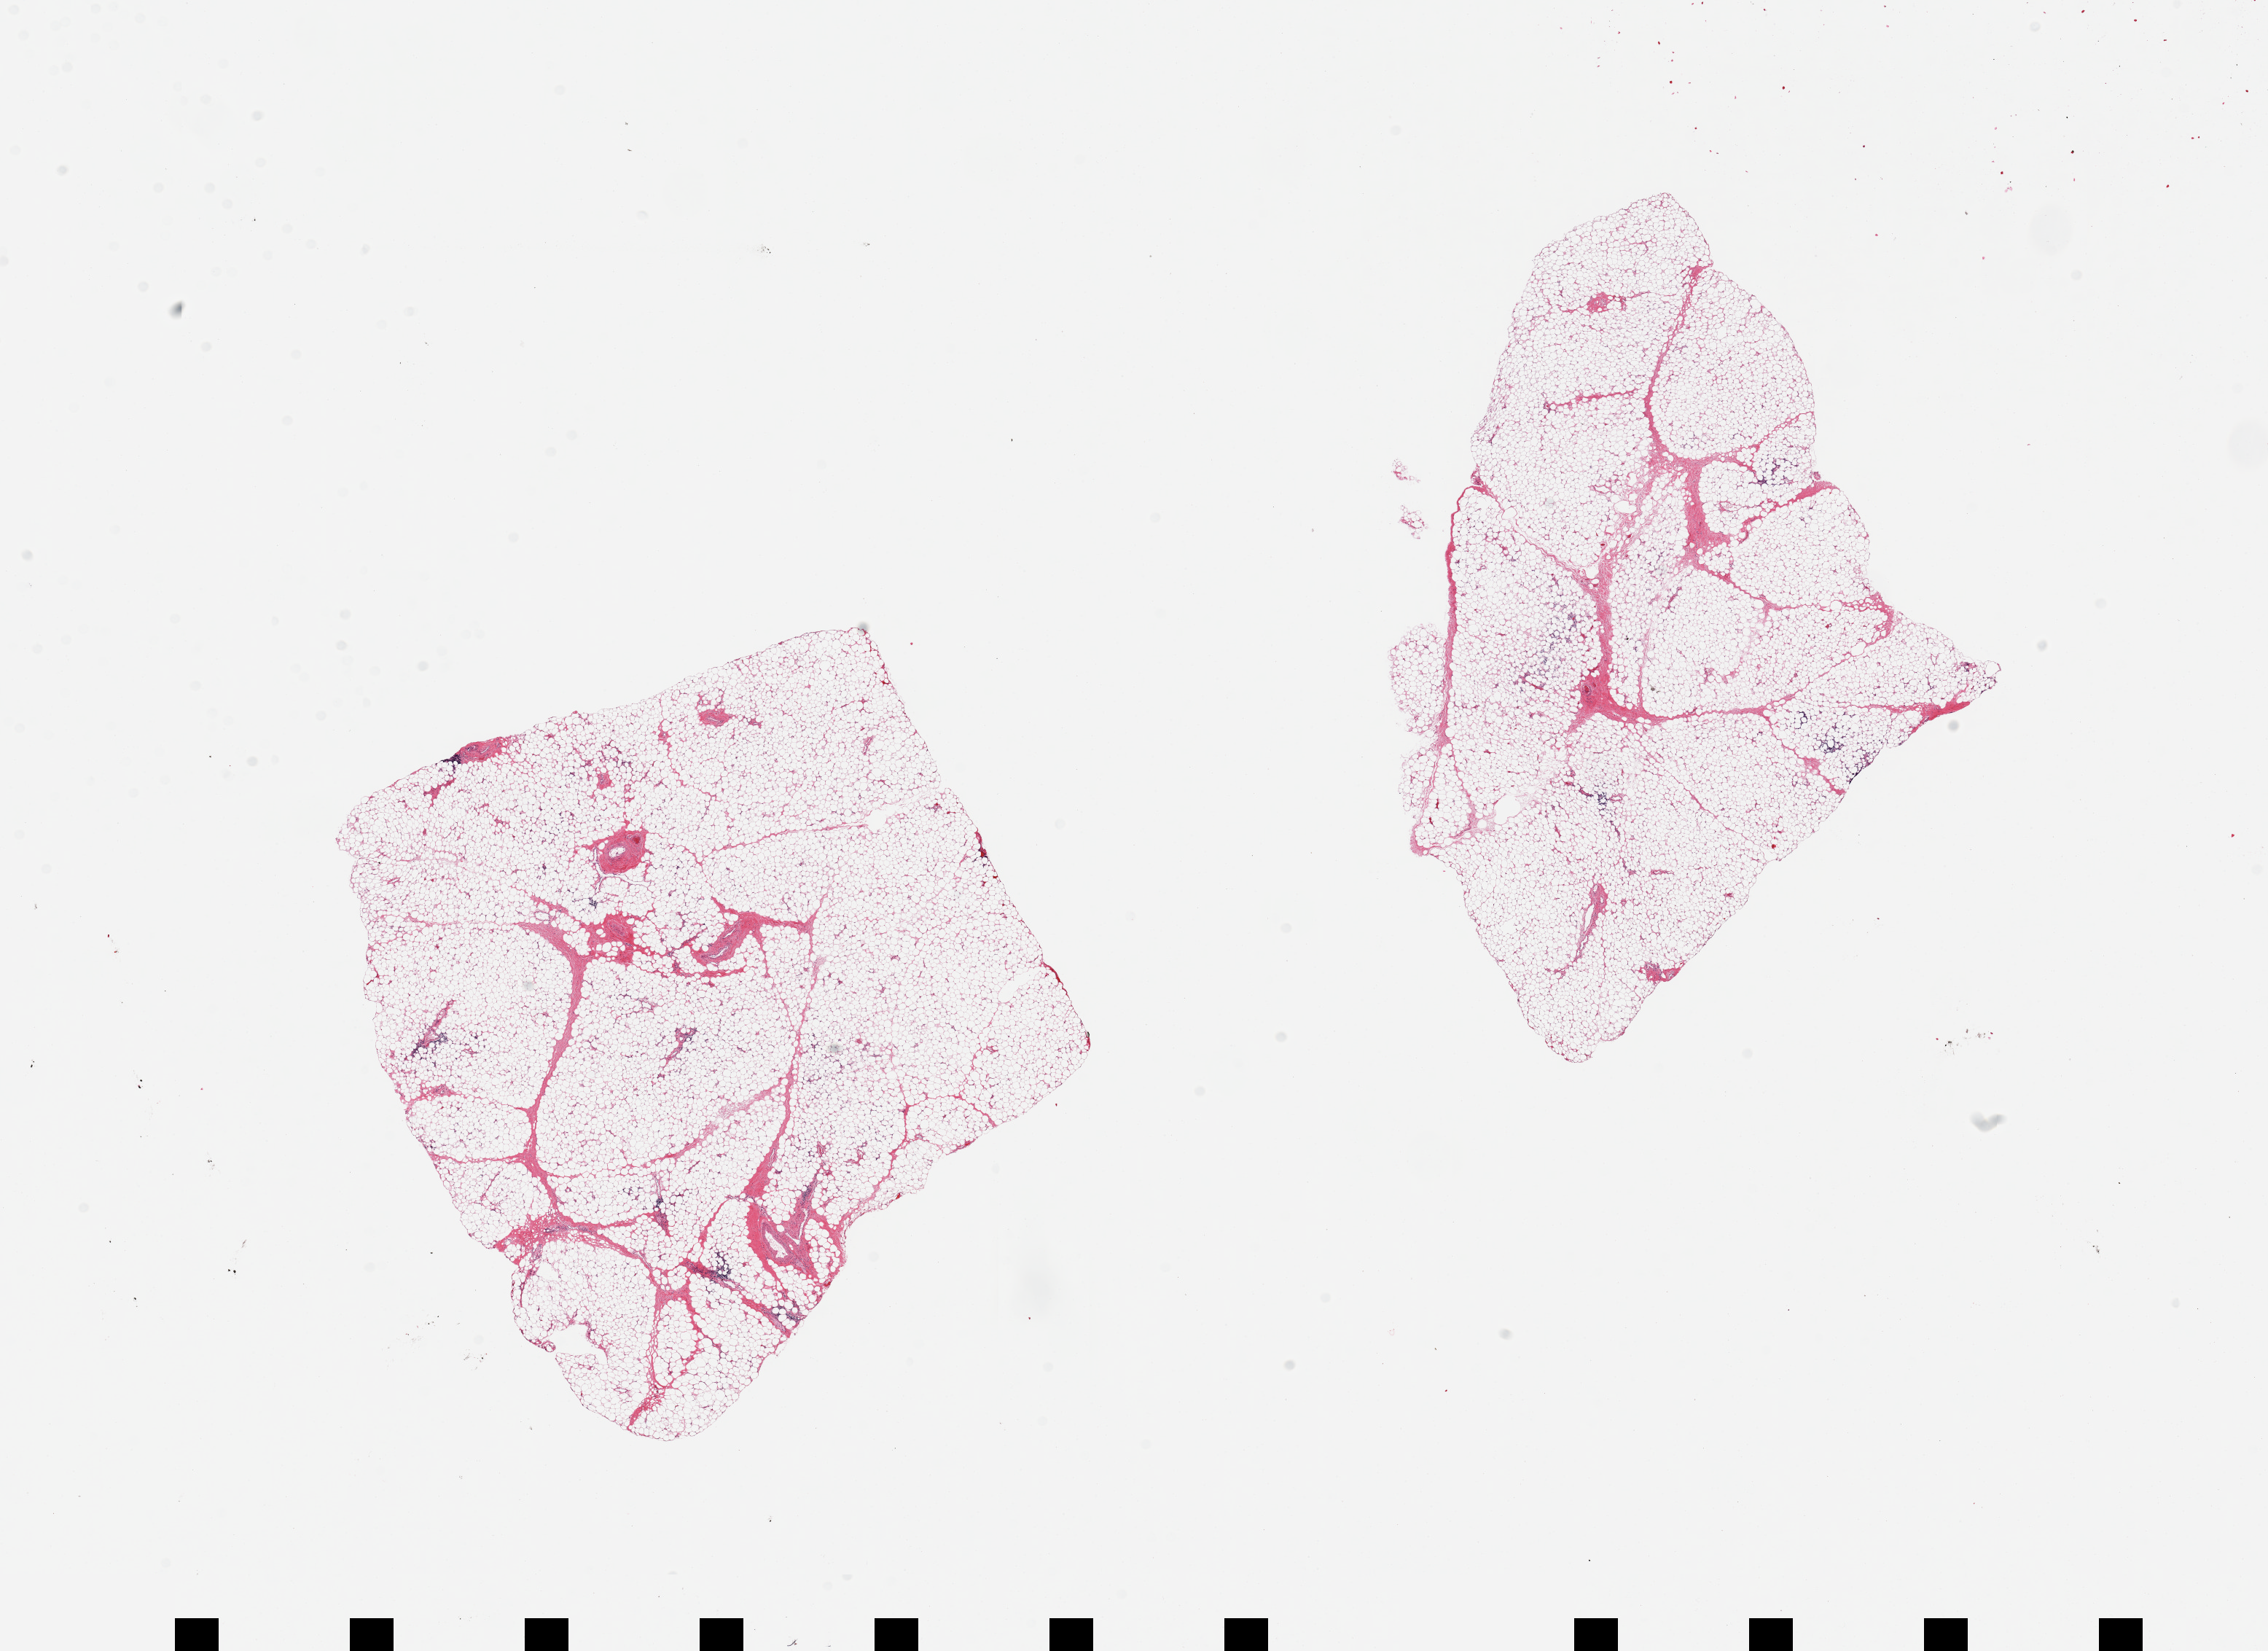
Digitized H&E-stained section — low-resolution overview of the scanned area, about 24.6 x 17.9 mm. PAXgene-fixed paraffin-embedded (PFPE) section. Sampled site (target tissue): pancreas. Donor tissue sample.
Reviewer comment on this tissue sample: 2 pieces; fat, not pancreas.